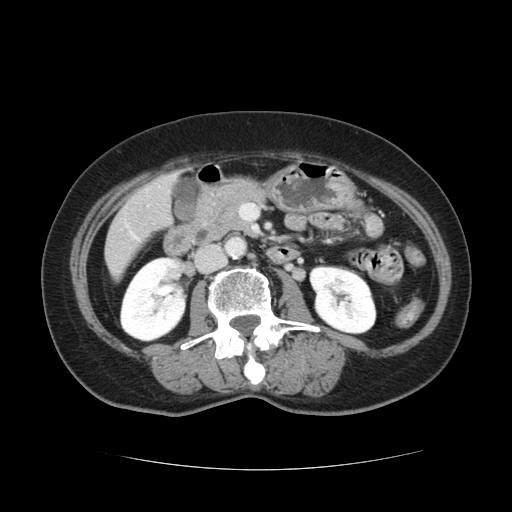
Contrast-enhanced abdominal CT, one axial slice. Slice 33 of 128 in the series (ordered by position). 120 kVp. Intravenous contrast given. Soft-tissue window (W 400 / L 40 HU). 512 × 512 image matrix. Female patient, age 67 years. Case-level facts recorded for this patient, not image findings: diagnosis: colorectal cancer liver metastases, imaged before liver resection; multiple liver metastases: yes; largest metastasis: 3 cm; disease in both lobes: yes.
Annotated regions visible in this slice (outlined manually by an expert reader):
- liver: bounding box [x1, y1, x2, y2] px = [105, 176, 175, 275]
- planned liver remnant (the part of the liver to remain after resection): [105, 215, 141, 275]